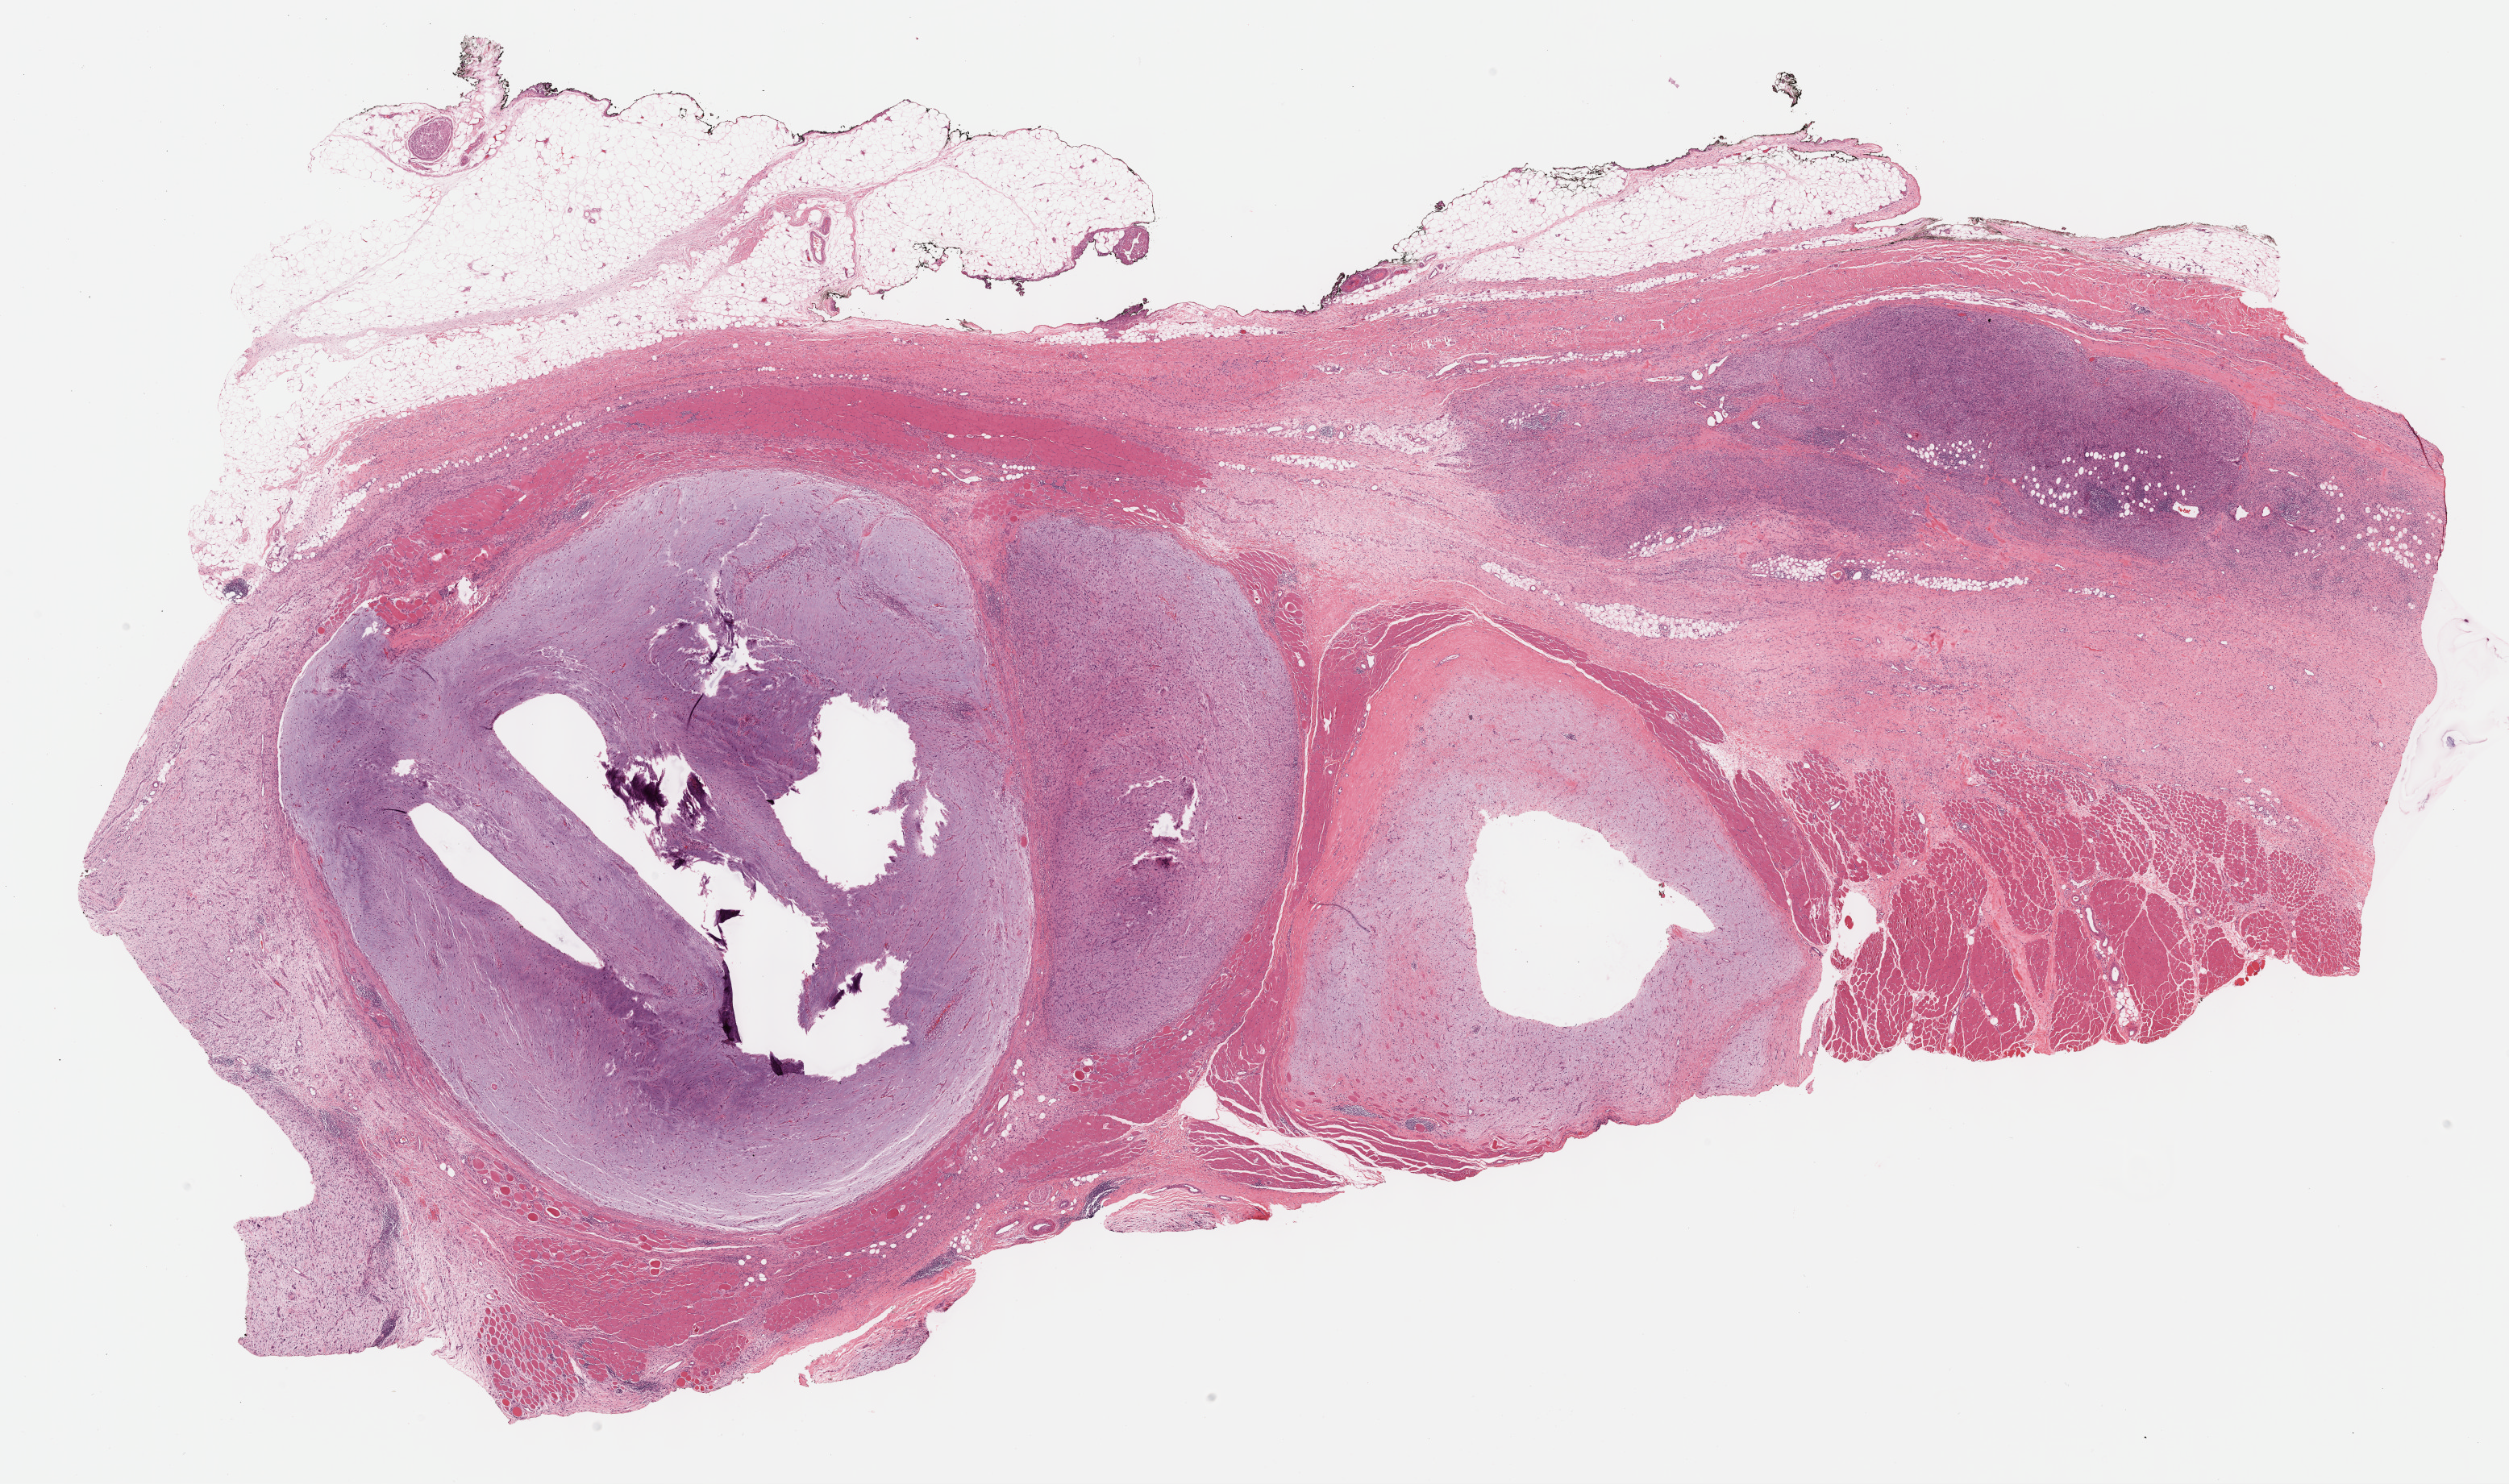
Hematoxylin and eosin (H&E) stained whole-slide image, whole scanned area (about 25.2 x 14.9 mm) shown as a low-resolution overview, formalin-fixed paraffin-embedded (FFPE) diagnostic section, primary tumour sample from the connective, subcutaneous and other soft tissues. Female patient; age at initial diagnosis 78 years.
Pathologic diagnosis: Fibromyxosarcoma (connective, subcutaneous and other soft tissues of lower limb and hip).